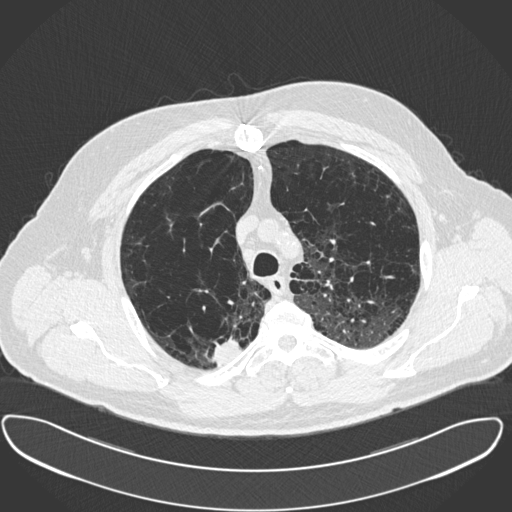
Low-dose screening chest CT, one axial slice; position 302 of 385 along the scan axis; reconstruction kernel B30f; 120 kVp; lung window (W 1500 / L -600 HU); 1 mm slice thickness; 512 × 512 image matrix, field of view 408 × 408 mm.
Annotated regions visible in this slice (manually delineated by an expert):
- lesion 1 (tumor, upper lobe of right lung): bounding box [x1, y1, x2, y2] px = [210, 339, 241, 365]